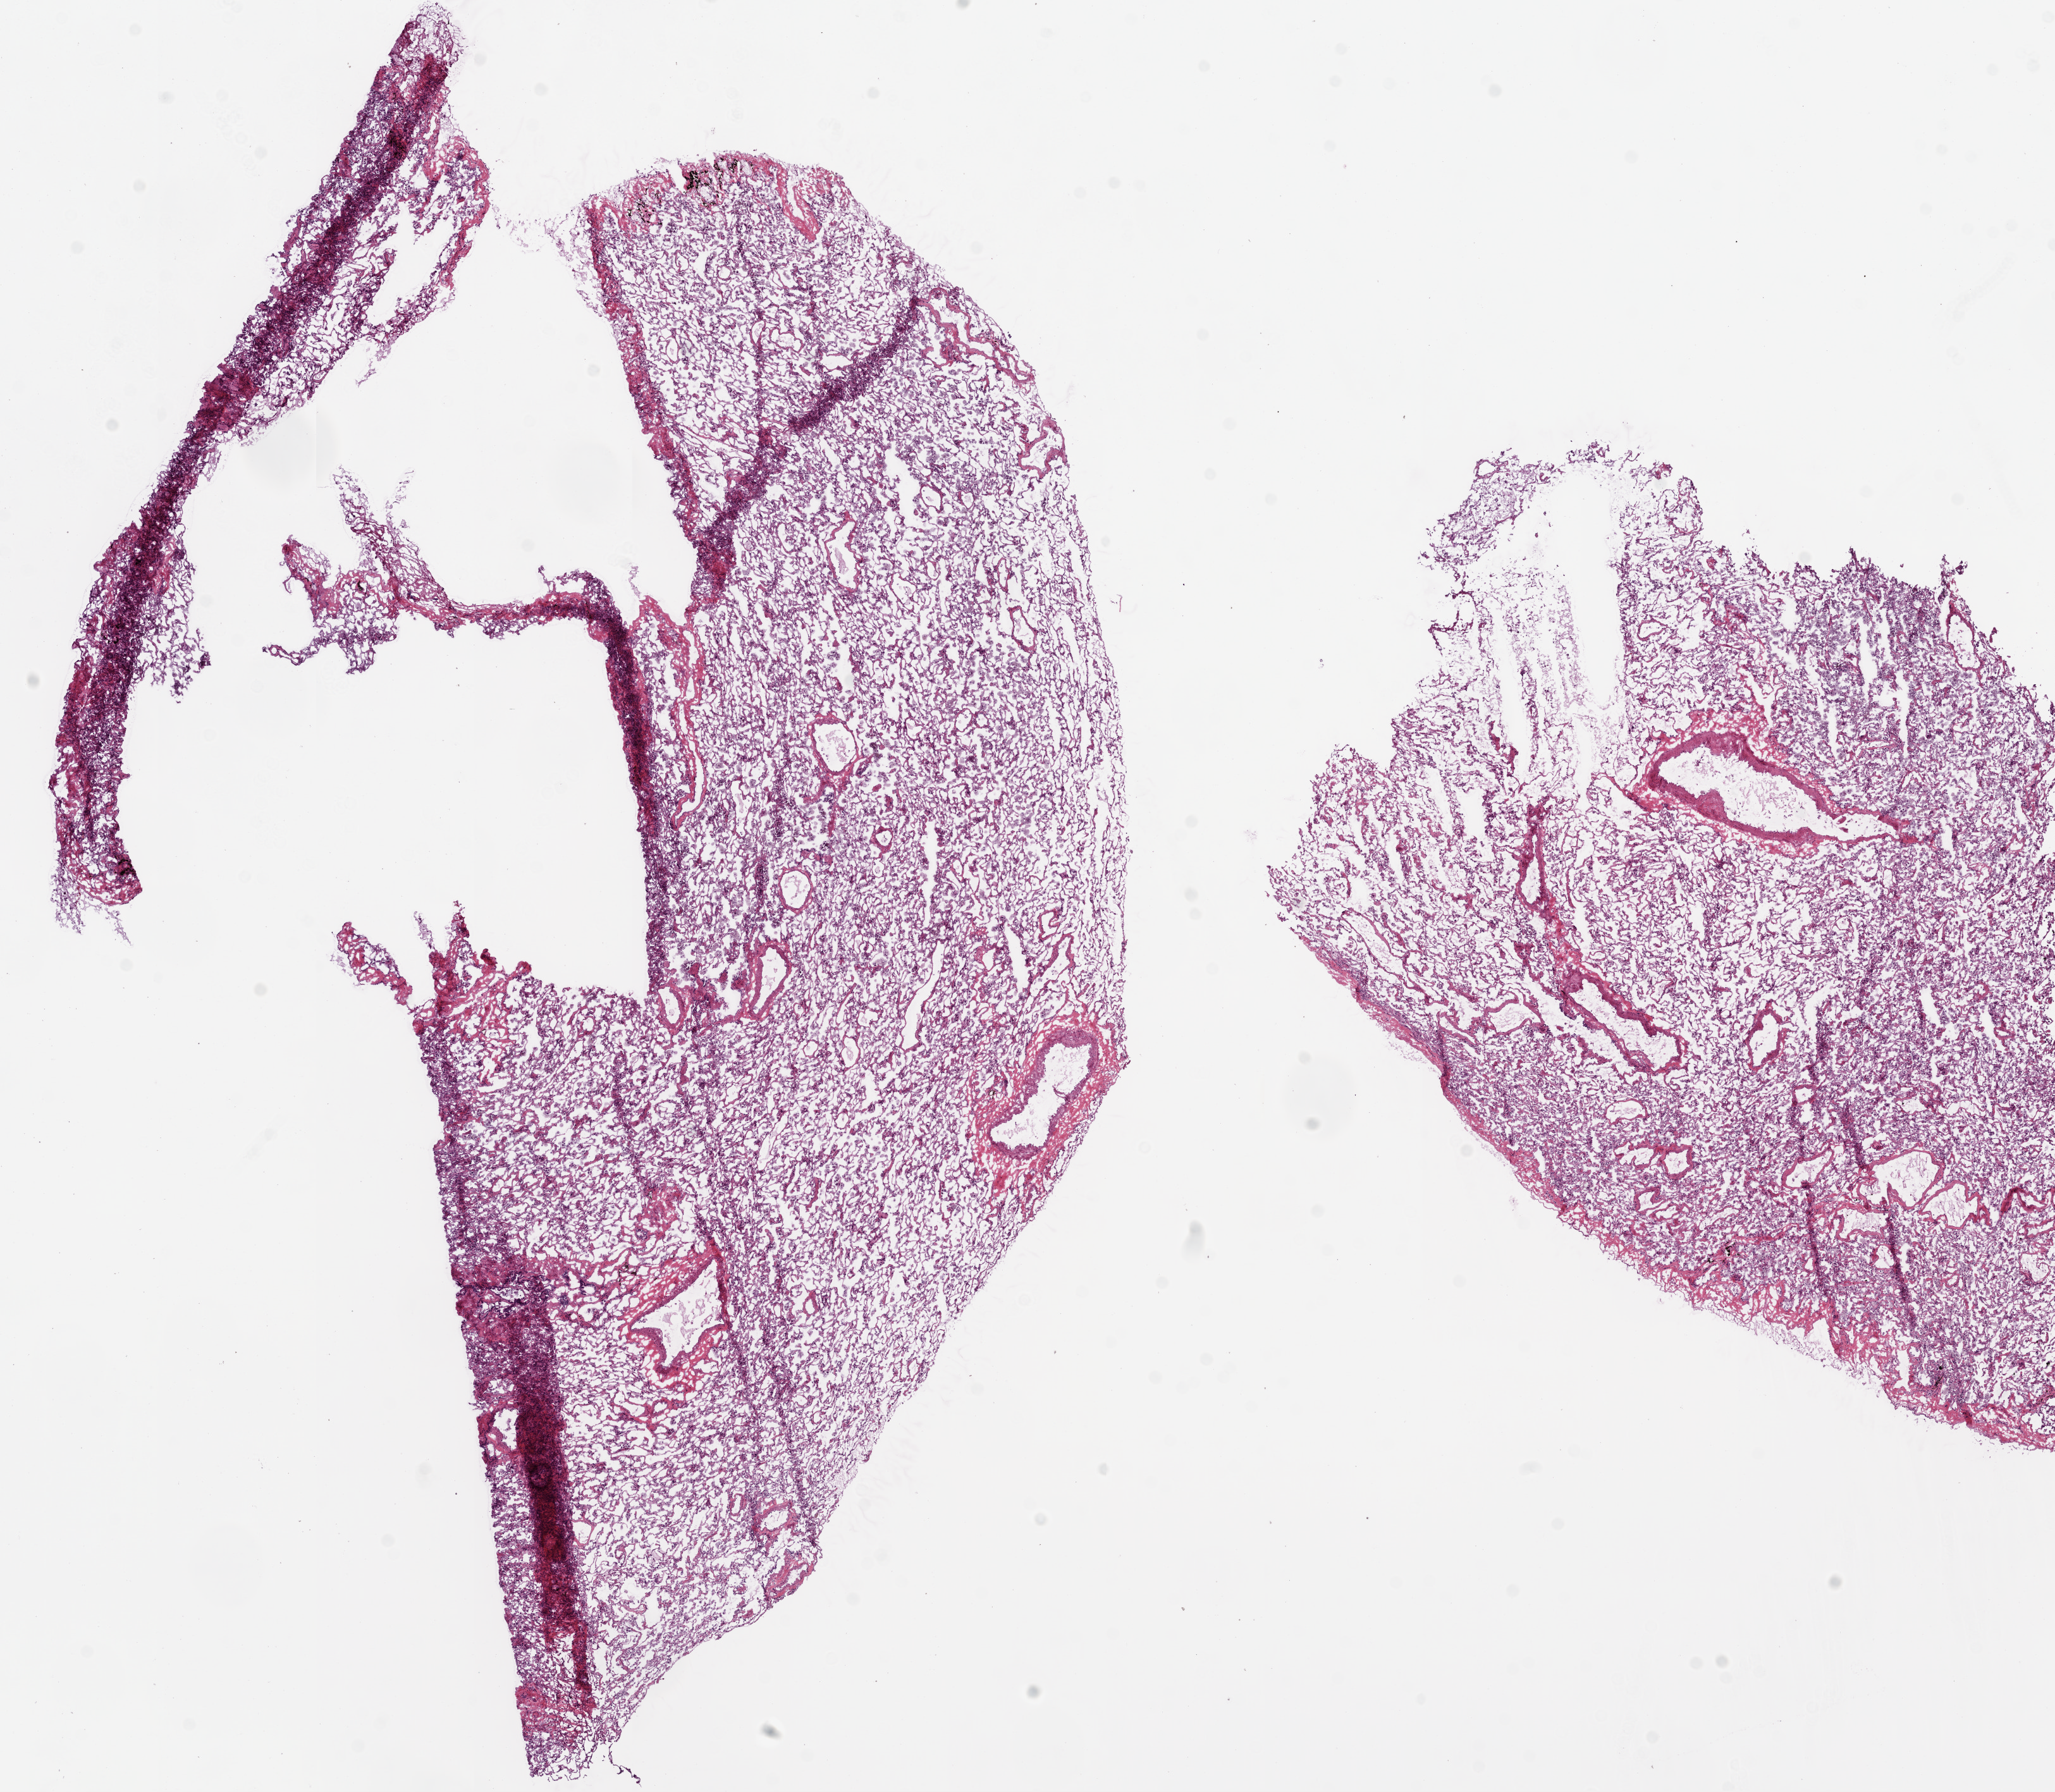
Whole-slide histology image, H&E — whole scanned area (about 13.0 x 11.4 mm) shown as a low-resolution overview; frozen section; lung, solid tissue normal (non-tumour tissue) sample. Patient: male, age at initial diagnosis 40 years.
* this section: solid tissue normal sample (biorepository sample class)
* patient diagnosis: Squamous cell carcinoma, NOS (upper lobe, lung)